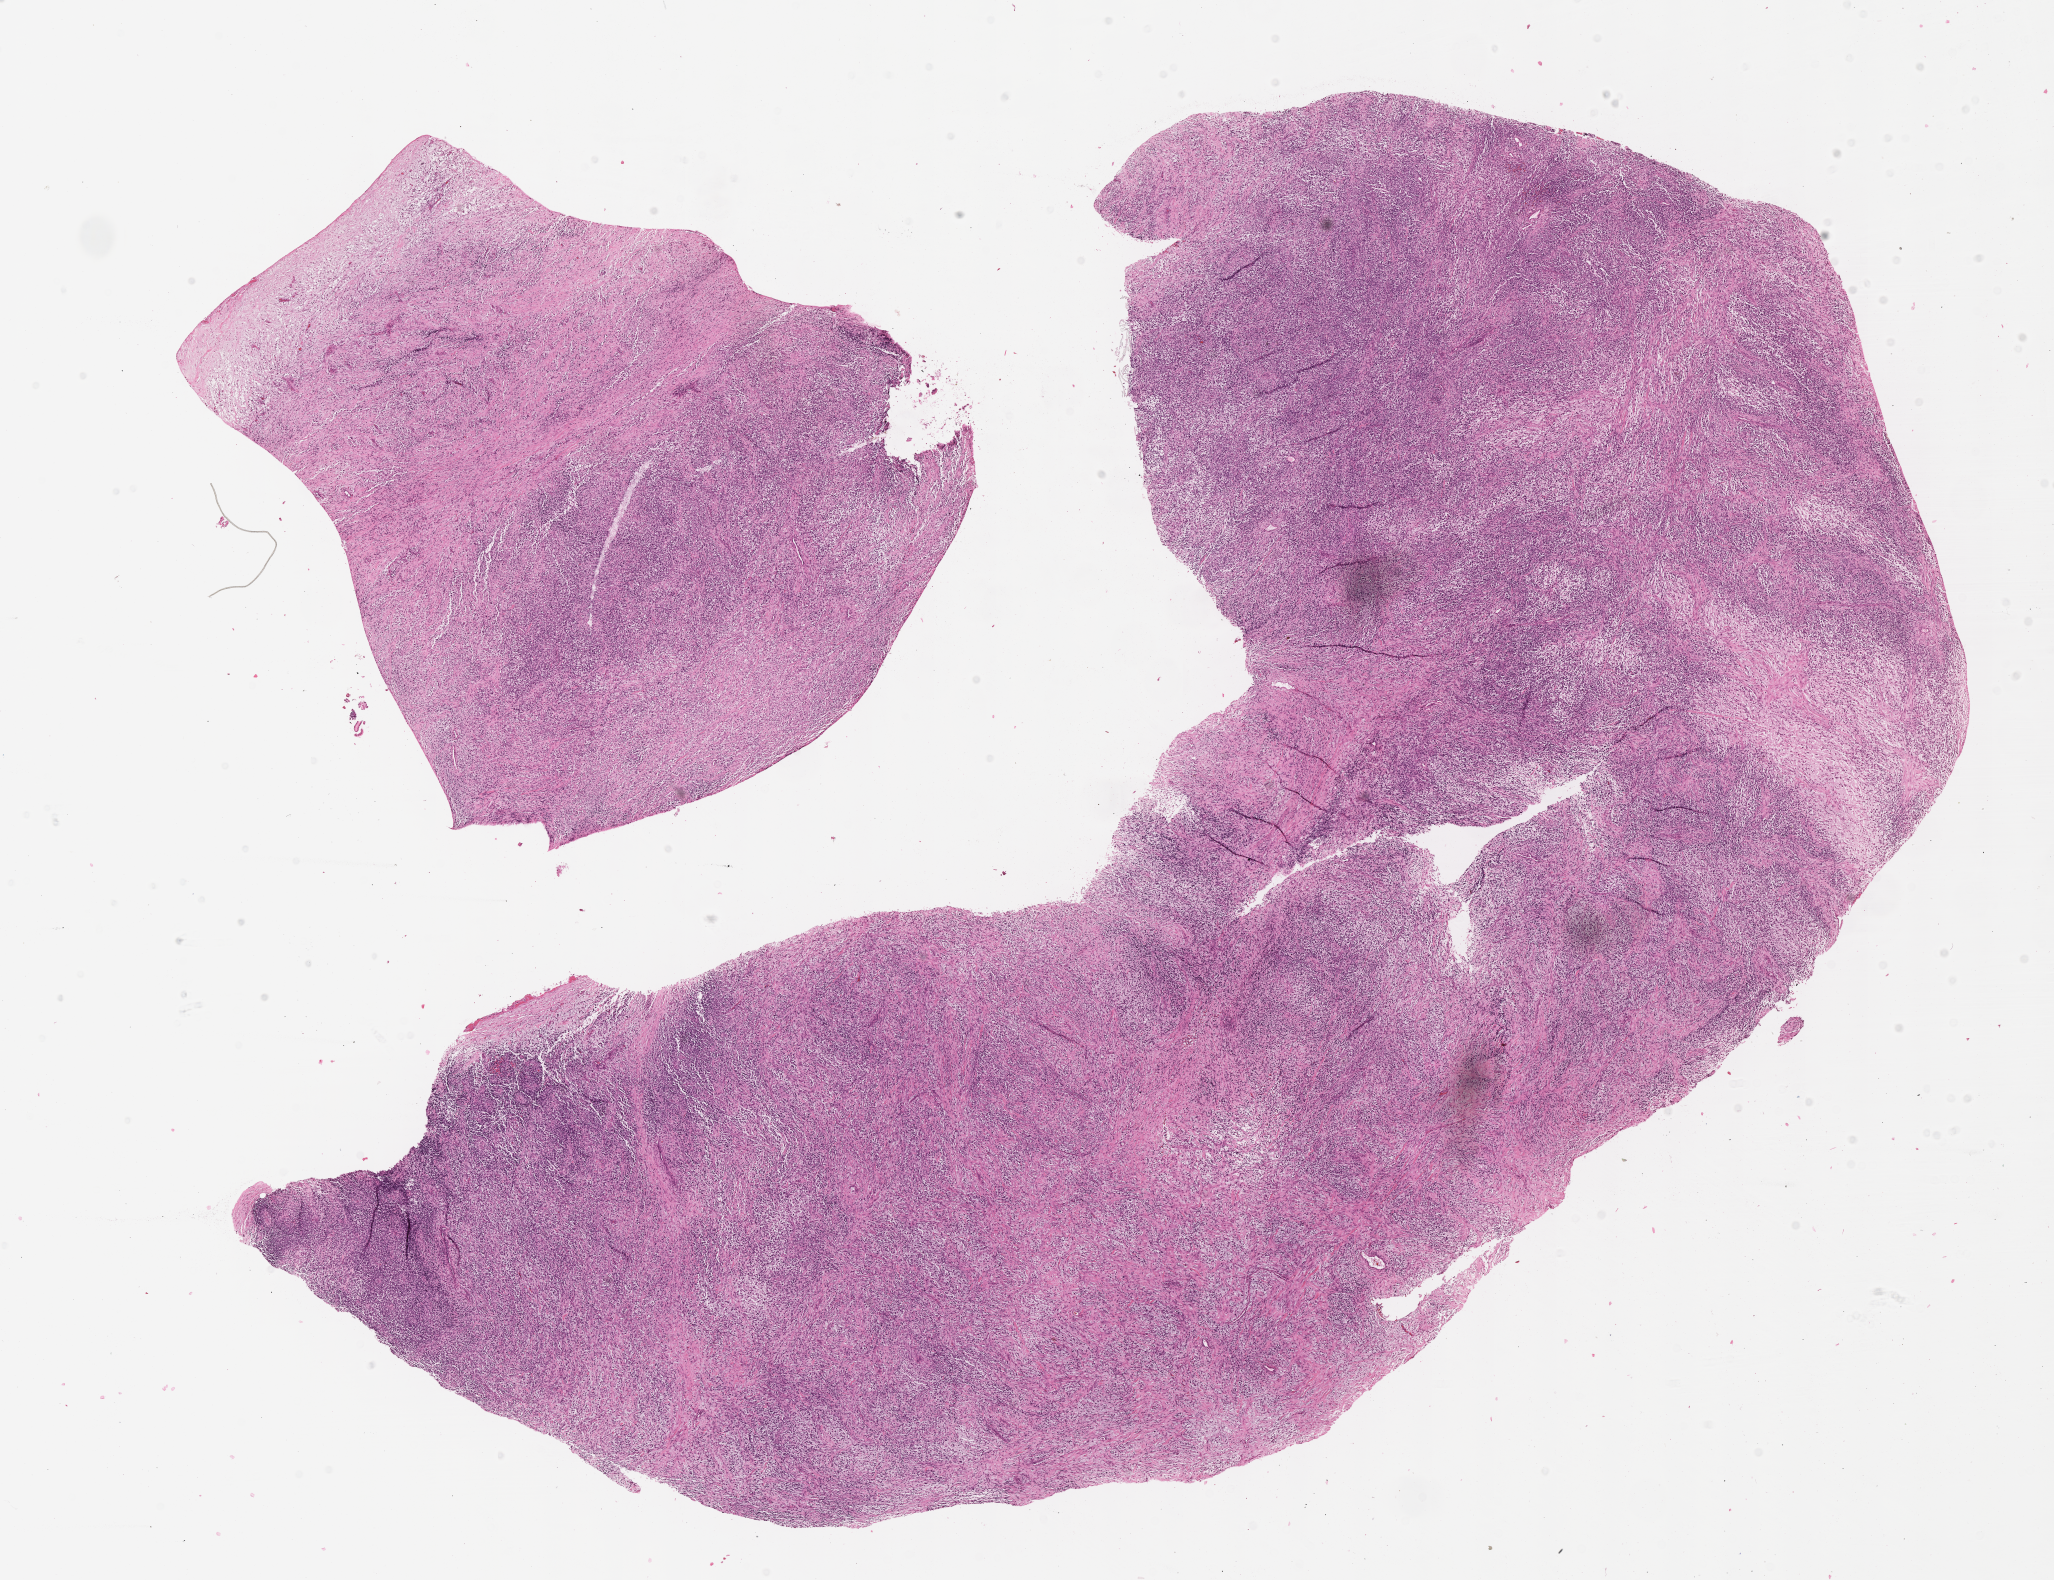
H&E whole-slide image of tumor tissue, a low-resolution overview of the entire scanned area, about 16.6 x 12.8 mm, FFPE section, sample anatomic site: abdomen. Male patient, age at diagnosis 2.0 years.
Stage (as recorded): 4. Metastatic status at presentation (as recorded): metastatic (confirmed). Primary site (case record): stomach. Diagnosis: rhabdomyosarcoma; histological classification: embryonal rhabdomyosarcoma.